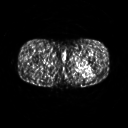
FDG PET of an extremity soft-tissue mass (from a PET/CT study), one axial slice; 128 × 128 image matrix. Patient: male, 27 years. From the clinical record (not read from this slice): histological type: extraskeletal osteosarcoma; grade: high; site of the primary tumour: left adductur.
Structures marked on this image (expert contour drawn on MRI and transferred to this co-registered scan by the dataset authors):
- gross tumour volume (mass): bounding box [x1, y1, x2, y2] px = [71, 60, 95, 75]